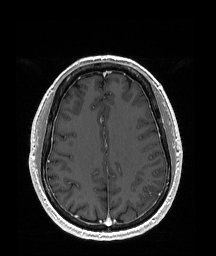
Brain MRI from a brain-tumour surgery series, one axial slice. Slice 72 of 192 in the series (ordered by position). T1-weighted post-contrast. 1 mm slice thickness. 216 × 256 image matrix. From the clinical record (not read from this slice): histopathology: Glioblastoma; WHO grade: 4; IDH mutation: no.
Annotated regions visible in this slice (expert manual segmentation):
- tumour: bounding box (x1, y1, x2, y2) in pixels: (143, 185, 159, 205)